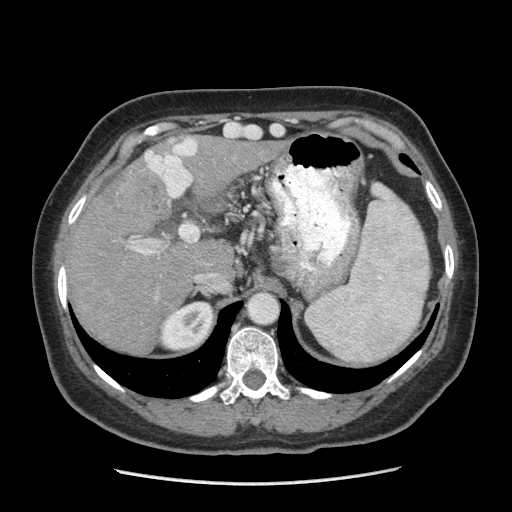
Contrast-enhanced abdominal CT (liver protocol), one axial slice; position 157 of 185 along the scan axis; 140 kVp; soft-tissue window (W 400 / L 40 HU); 2.5 mm slice thickness; 512 × 512 image matrix, field of view 360 × 360 mm. Case-level facts recorded for this patient, not image findings: diagnosis: hepatocellular carcinoma (patient treated with transarterial chemoembolisation; whether this scan precedes or follows treatment is not stated here); TNM stage (as recorded): Stage-I; Child-Pugh class: A.
Outlined on this slice (semi-automatically segmented with operator editing):
- liver parenchyma outside the tumour (the mass and vessels are separate outlines, so this box may not span the whole liver): box from (x=66, y=136) to (x=274, y=352) px
- mass: (x=113, y=164)–(x=169, y=225)
- liver vessels: (x=131, y=138)–(x=197, y=255)